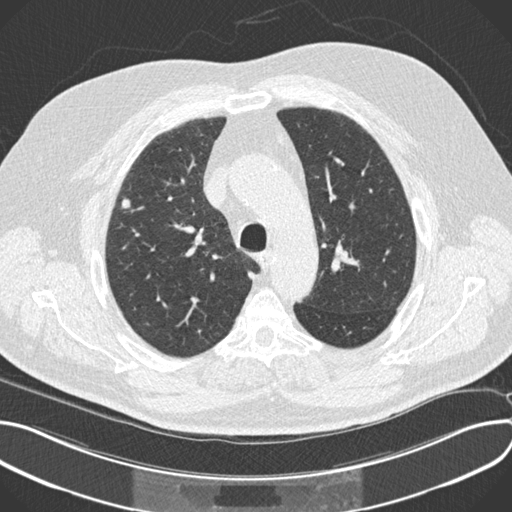
Chest CT (low-dose screening protocol), one axial image; third annual screen; lung window (W 1500 / L -600 HU); 2 mm slice thickness; standard (soft-tissue) reconstruction kernel (B30f); slice 55 of 212 in the series; 512 × 512 image matrix. Male participant, aged 64 years at enrolment.
Expert reader's lesion annotation, bounding box [x1, y1, x2, y2] px = [108, 187, 142, 223]. Screening reader's record for this exam (one nodule recorded; not confirmed to be the boxed lesion): non-calcified nodule or mass ≥4 mm, right upper lobe, 7 × 6 mm, smooth margins, soft tissue attenuation, pre-existing on the prior screen: no. Official screen result: positive, other. Participant outcome: lung cancer diagnosed 104 days after this screen — squamous cell carcinoma, NOS, right upper lobe, moderately differentiated (G2), stage IA (AJCC 6th edition), 7 mm at pathology.